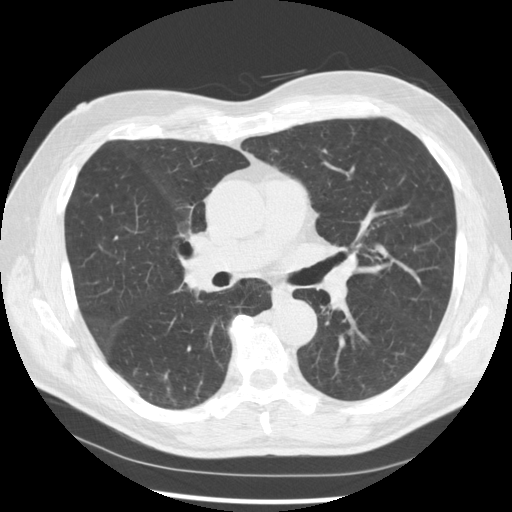
Low-dose screening chest CT, one axial slice. Slice 161 of 277 in the series (ordered by position). Reconstruction kernel STANDARD. 120 kVp. Lung window (W 1500 / L -600 HU). 512 × 512 image matrix, field of view 365 × 365 mm.
Structures marked on this image (manually delineated by an expert):
- lesion 1 (tumor, middle lobe of right lung): bounding box <181,256,215,295> (left, top, right, bottom; pixels)